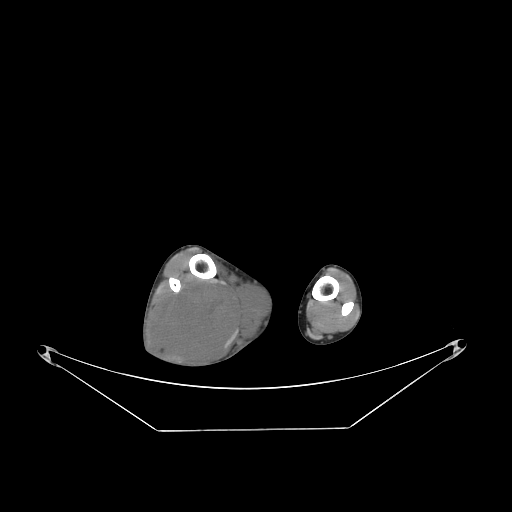
CT of an extremity soft-tissue mass (from a PET/CT study), one axial slice. Slice 68 of 267 in the series (ordered by position). Reconstruction kernel STANDARD. Soft-tissue window (W 400 / L 40 HU). 3.75 mm slice thickness. 512 × 512 image matrix, field of view 500 × 500 mm. Male patient. Case-level facts recorded for this patient, not image findings: histological type: liposarcoma - round cell; grade: high; site of the primary tumour: right calf.
Annotated regions visible in this slice (expert contour drawn on MRI and transferred to this co-registered scan by the dataset authors):
- gross tumour volume (mass): bounding box [x1, y1, x2, y2] px = [149, 274, 273, 369]